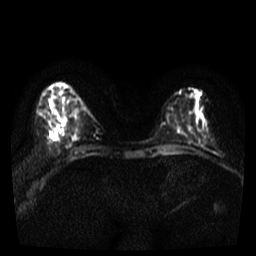
Breast MRI, one axial slice; position 11 of 36 along the scan axis; diffusion-weighted series; image 2 of 4 stored at this slice position (different b-values; order by instance number); 3 T; 5 mm slice thickness; 256 × 256 image matrix, field of view 300 × 300 mm. Female patient.
Structures marked on this image (manually delineated by an expert):
- tumour on diffusion-weighted imaging: box from (x=50, y=134) to (x=58, y=140) px